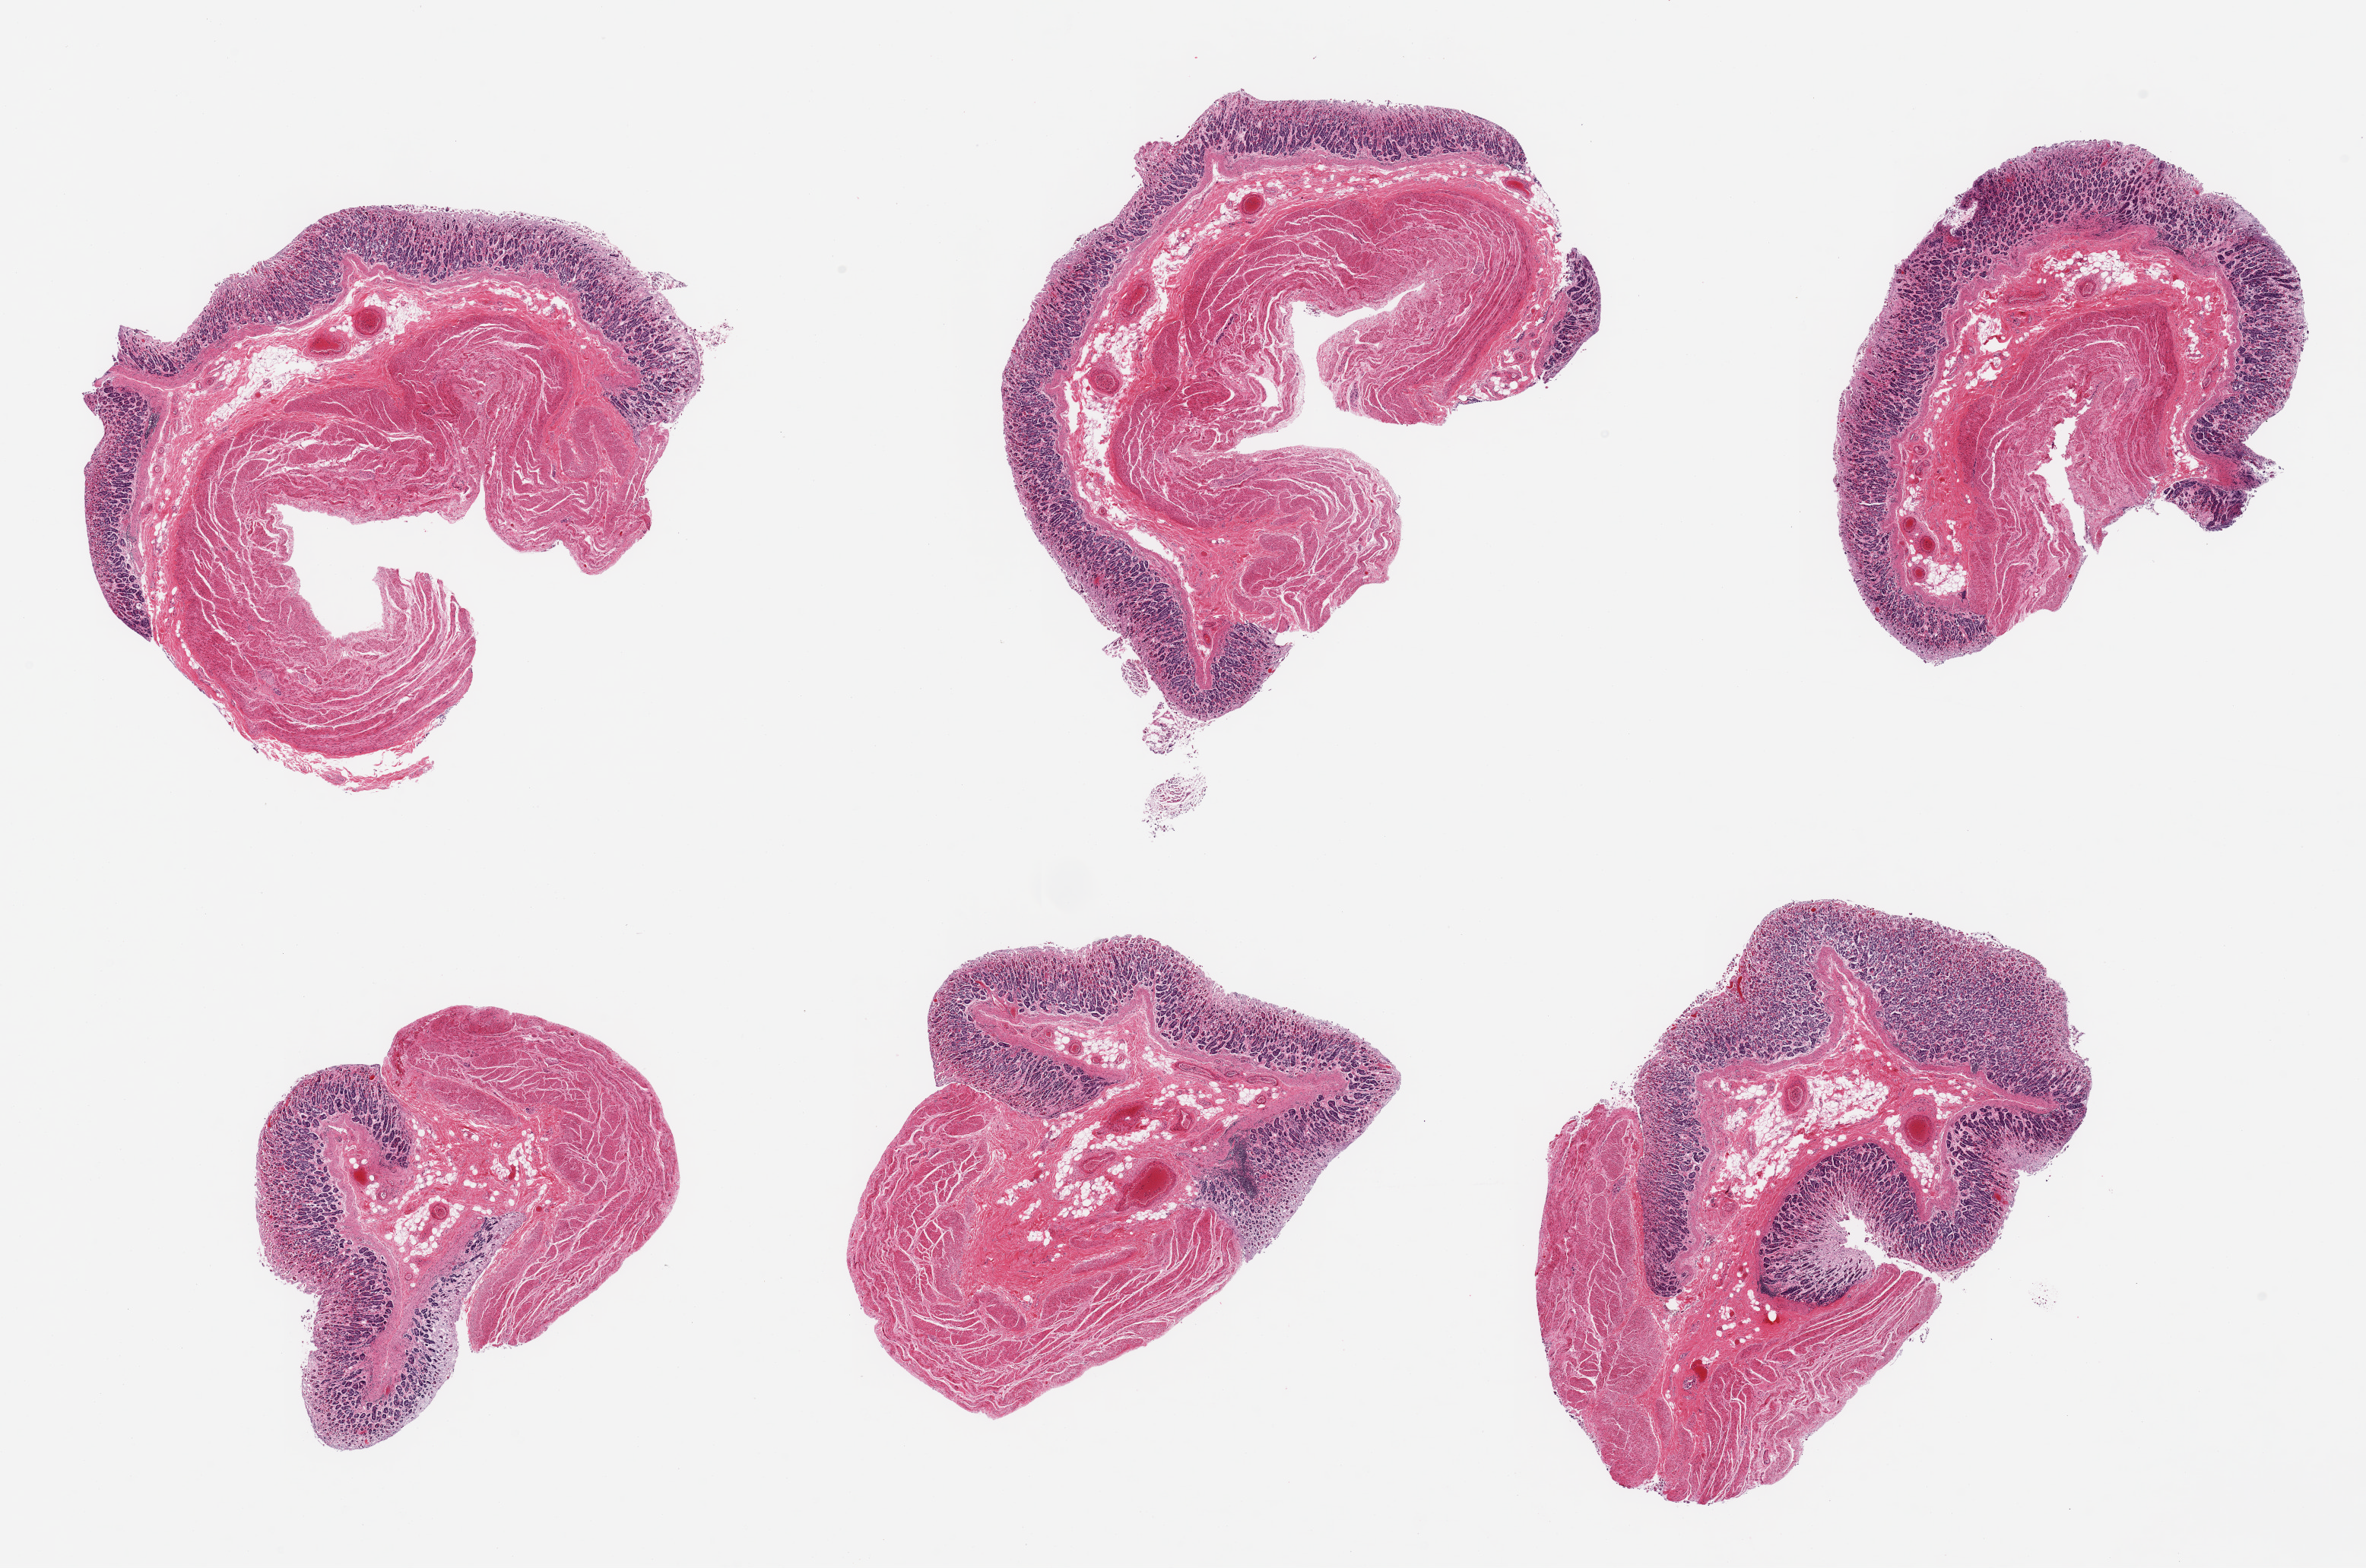
Whole-slide image, H&E stain, low-resolution overview of the scanned area, about 24.6 x 16.3 mm, PAXgene-fixed paraffin-embedded (PFPE) section, target tissue: stomach, donor tissue sample. Donor sex: female.
Pathologist's review note for this sample: 6 pieces; moderately autolyzed mucosa; intact muscularis.